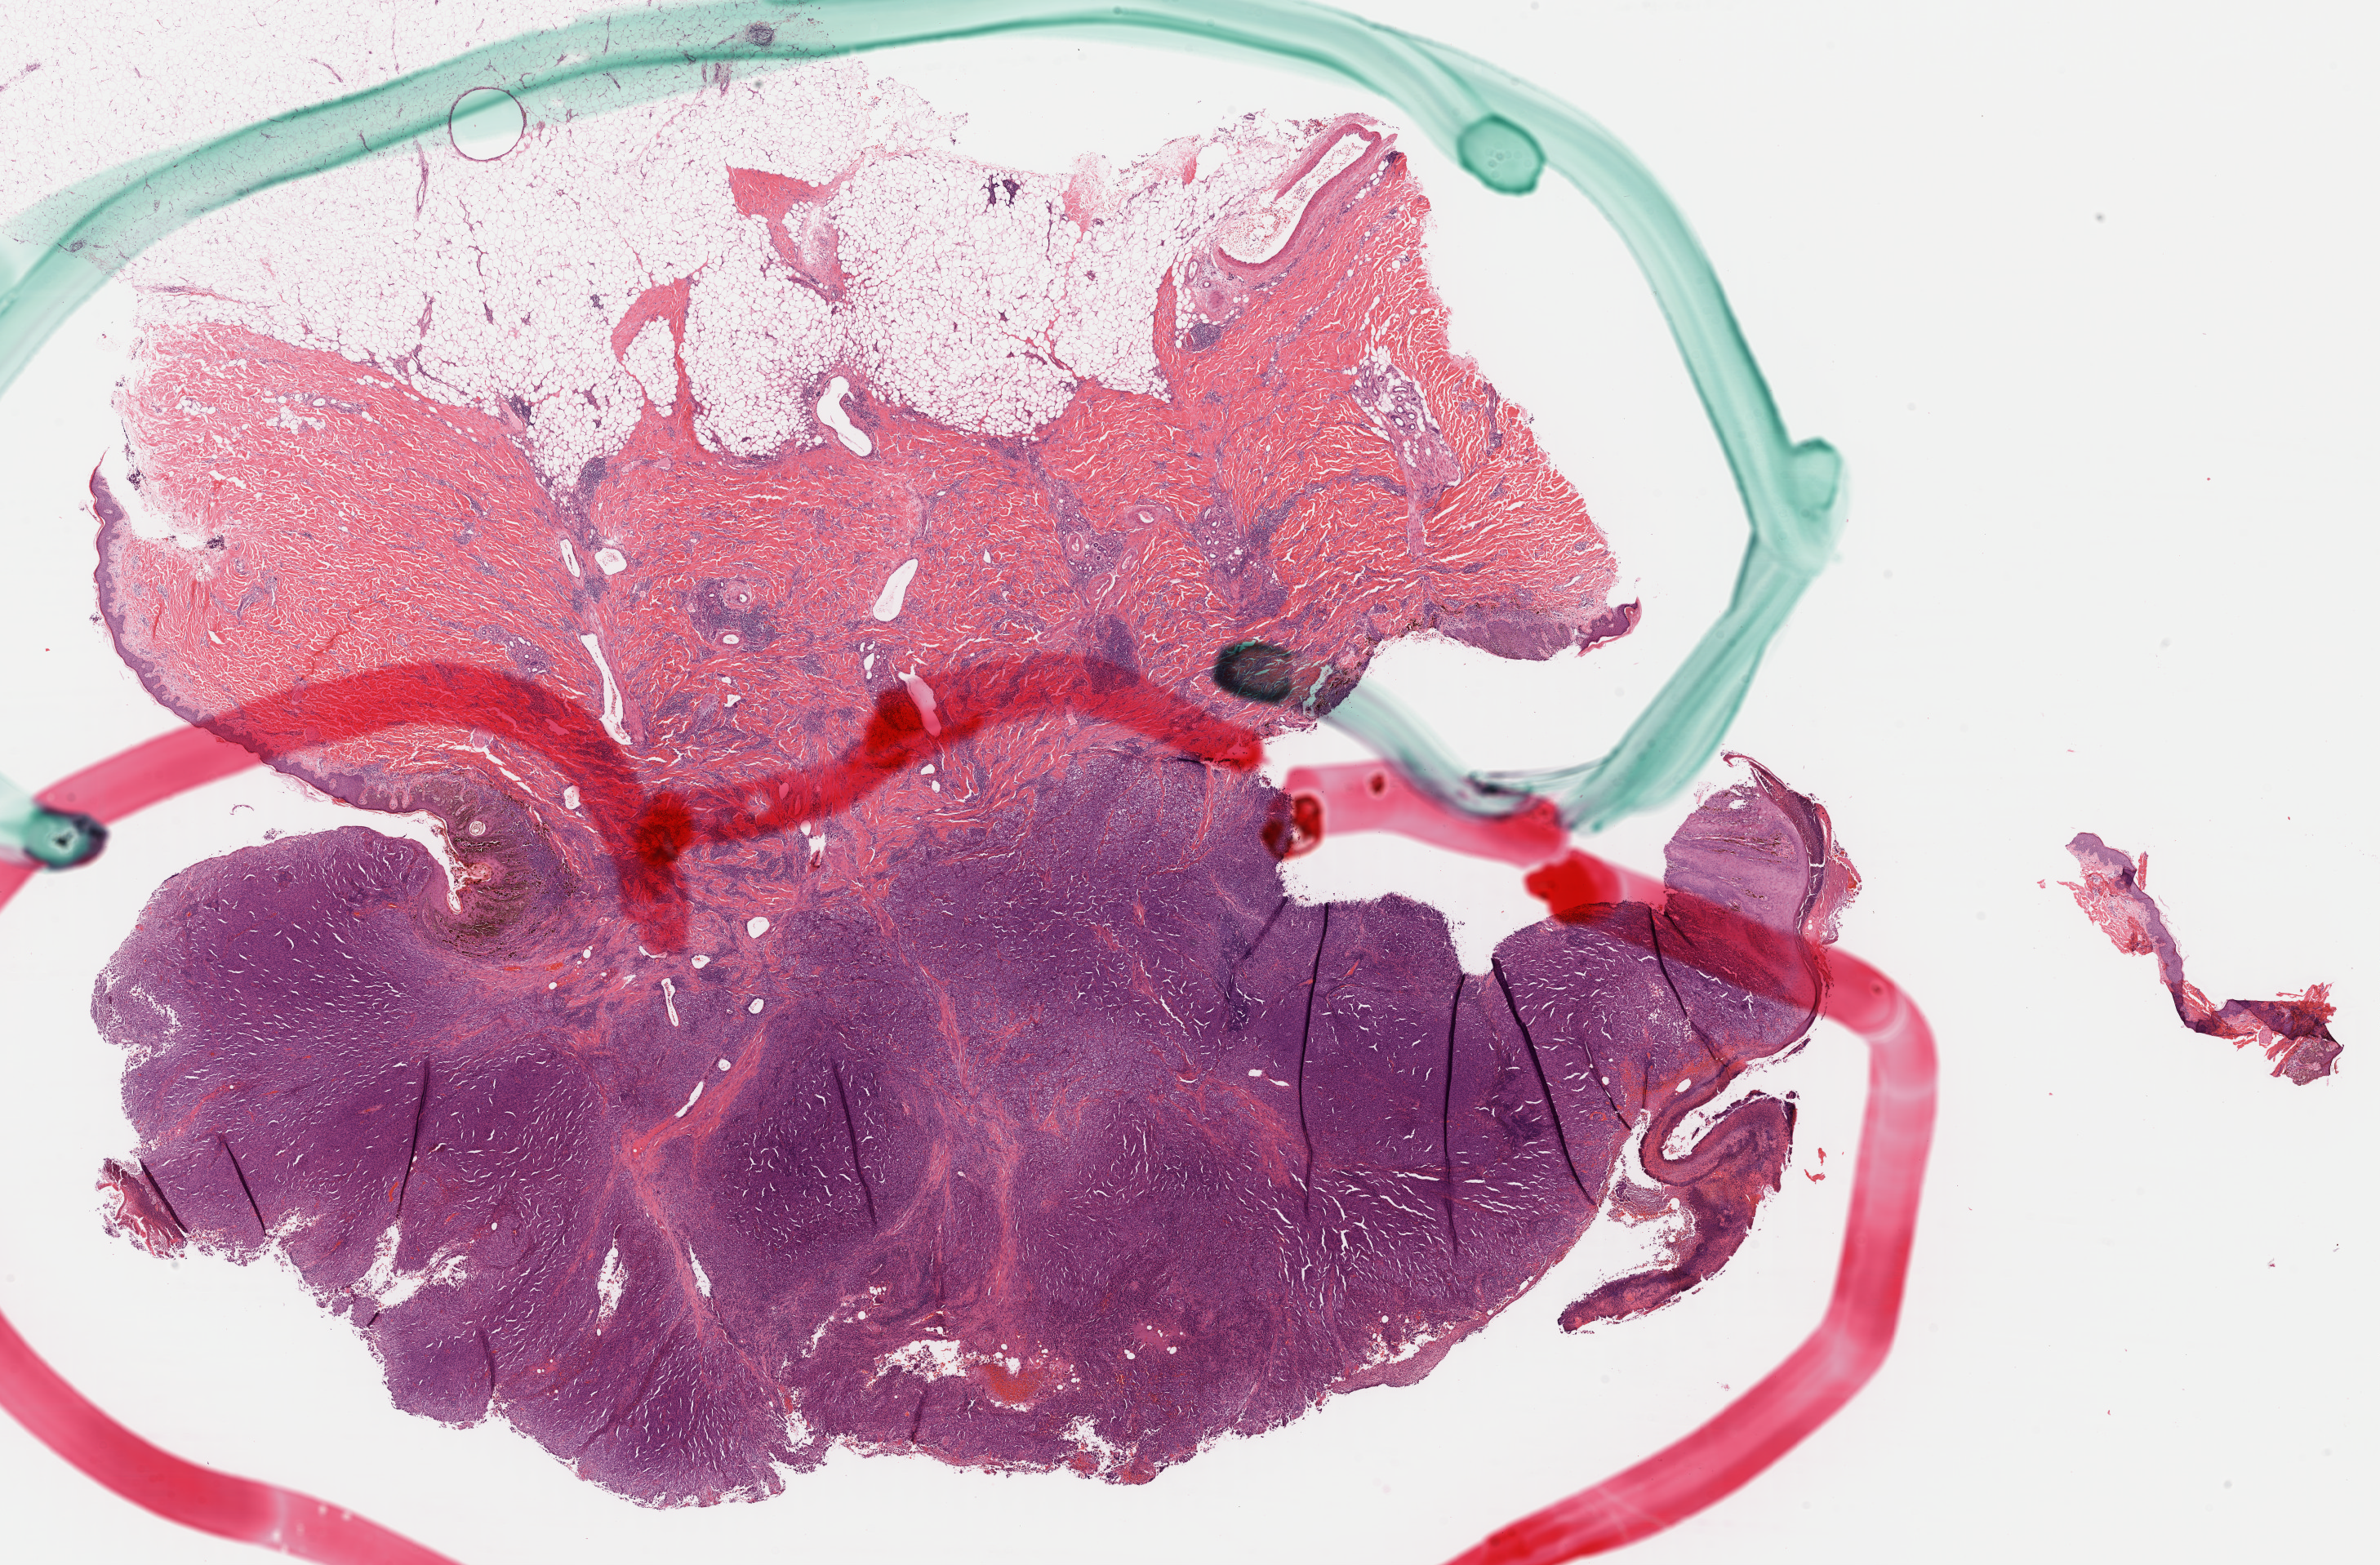
Digitized Hematoxylin and eosin (H&E) stained tissue section (whole slide) — shown as a low-resolution overview of the whole scanned area (about 23.0 x 15.1 mm, slide scanned at 40x). Formalin-fixed paraffin-embedded (FFPE) diagnostic section. Skin, primary tumour sample. Female, age 58 years at initial diagnosis.
AJCC pathologic stage: IIC. Diagnosis: Malignant melanoma, NOS.